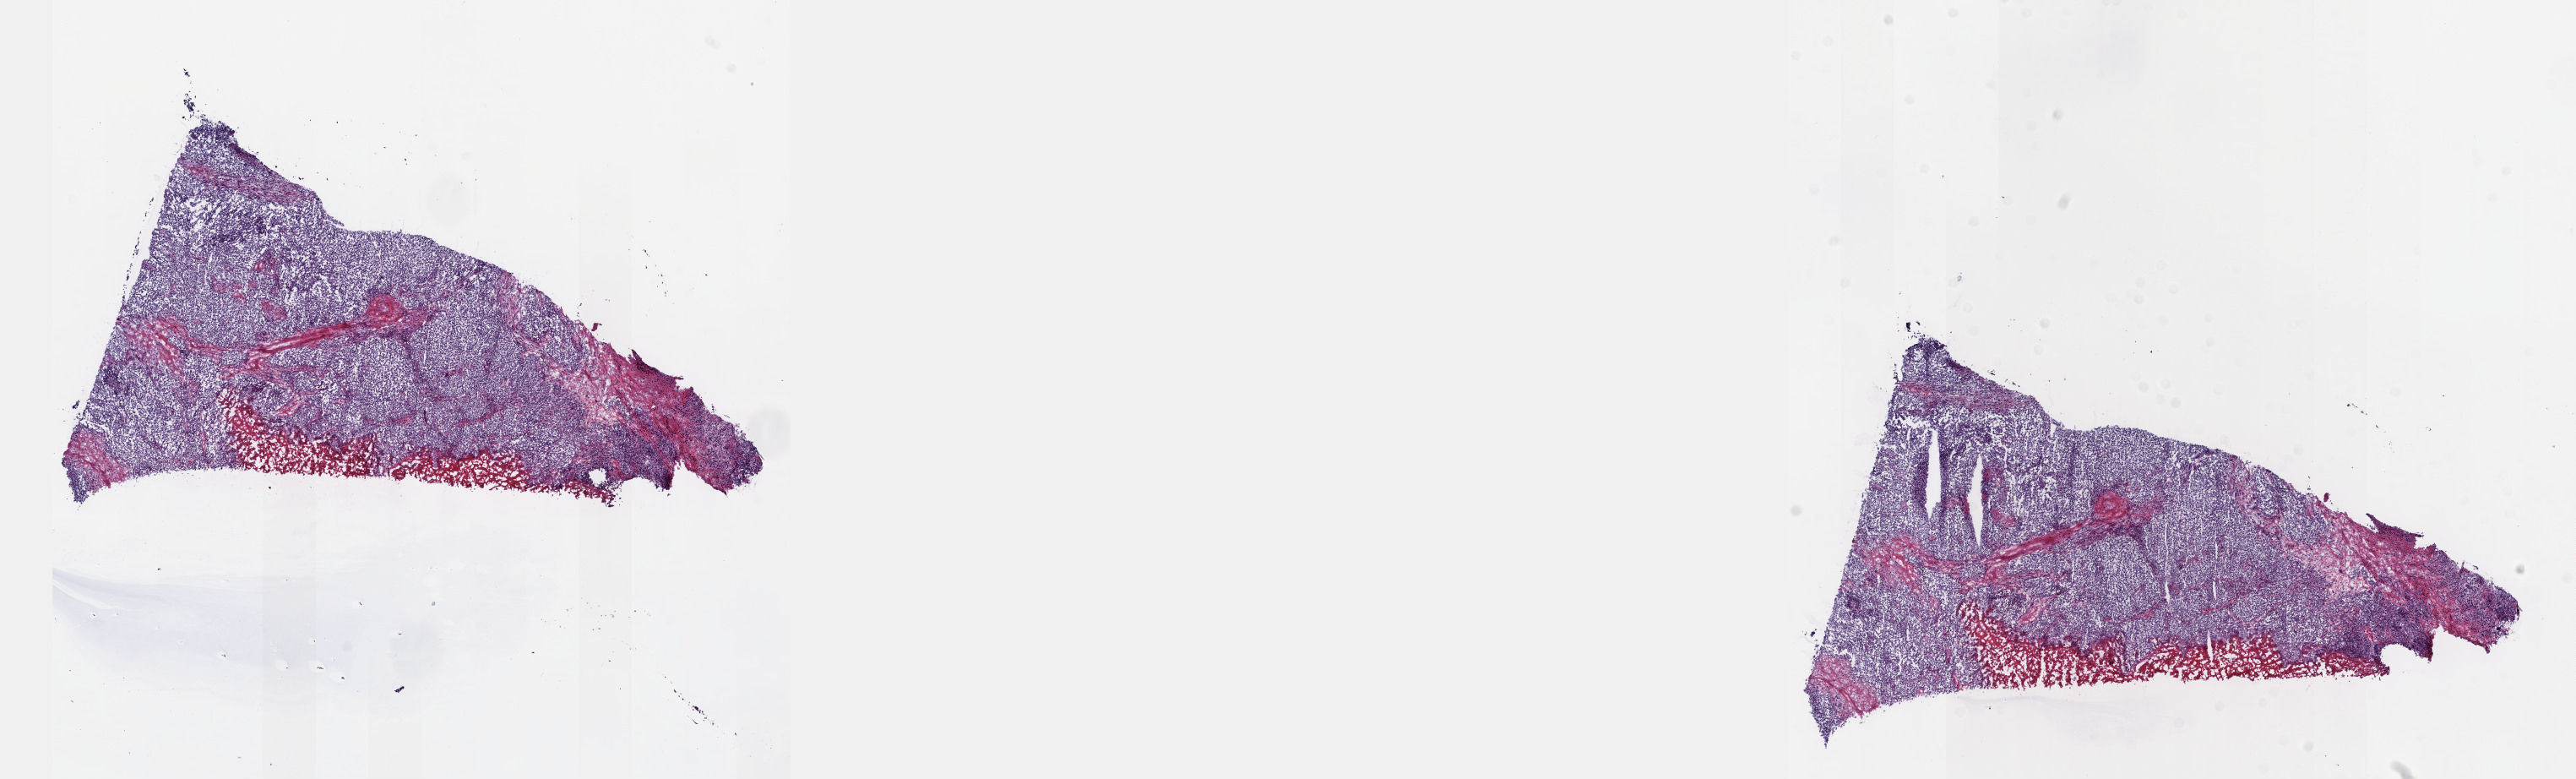
H&E whole-slide image — whole scanned area (about 24.6 x 7.5 mm, slide scanned at 40x) shown as a low-resolution overview. Frozen section from the top of the tissue portion. Sample: primary tumour, testis. Male patient; age at initial diagnosis 35 years. Composition of this section per pathologist review: tumour cells 85%, tumour nuclei 90%, normal cells 0%, stromal cells 15%, necrosis 0%. Inflammatory infiltration, as recorded: lymphocyte infiltration 0%, monocyte infiltration 0%, neutrophil infiltration 0%.
AJCC pathologic stage: IA (6th edition). Histologic diagnosis: Seminoma, NOS.